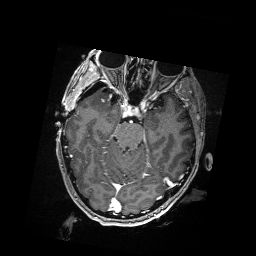
Brain MRI from a brain-tumour surgery series, one axial slice. Slice 114 of 176 in the series (ordered by position). T1-weighted post-contrast. 1 mm slice thickness. 256 × 256 image matrix. Case-level facts recorded for this patient, not image findings: histopathology: Metastatic Carcinoma from Breast primary.
Outlined on this slice (outlined manually by an expert reader):
- residual tumour: bounding box (x1, y1, x2, y2) in pixels: (98, 88, 110, 95)